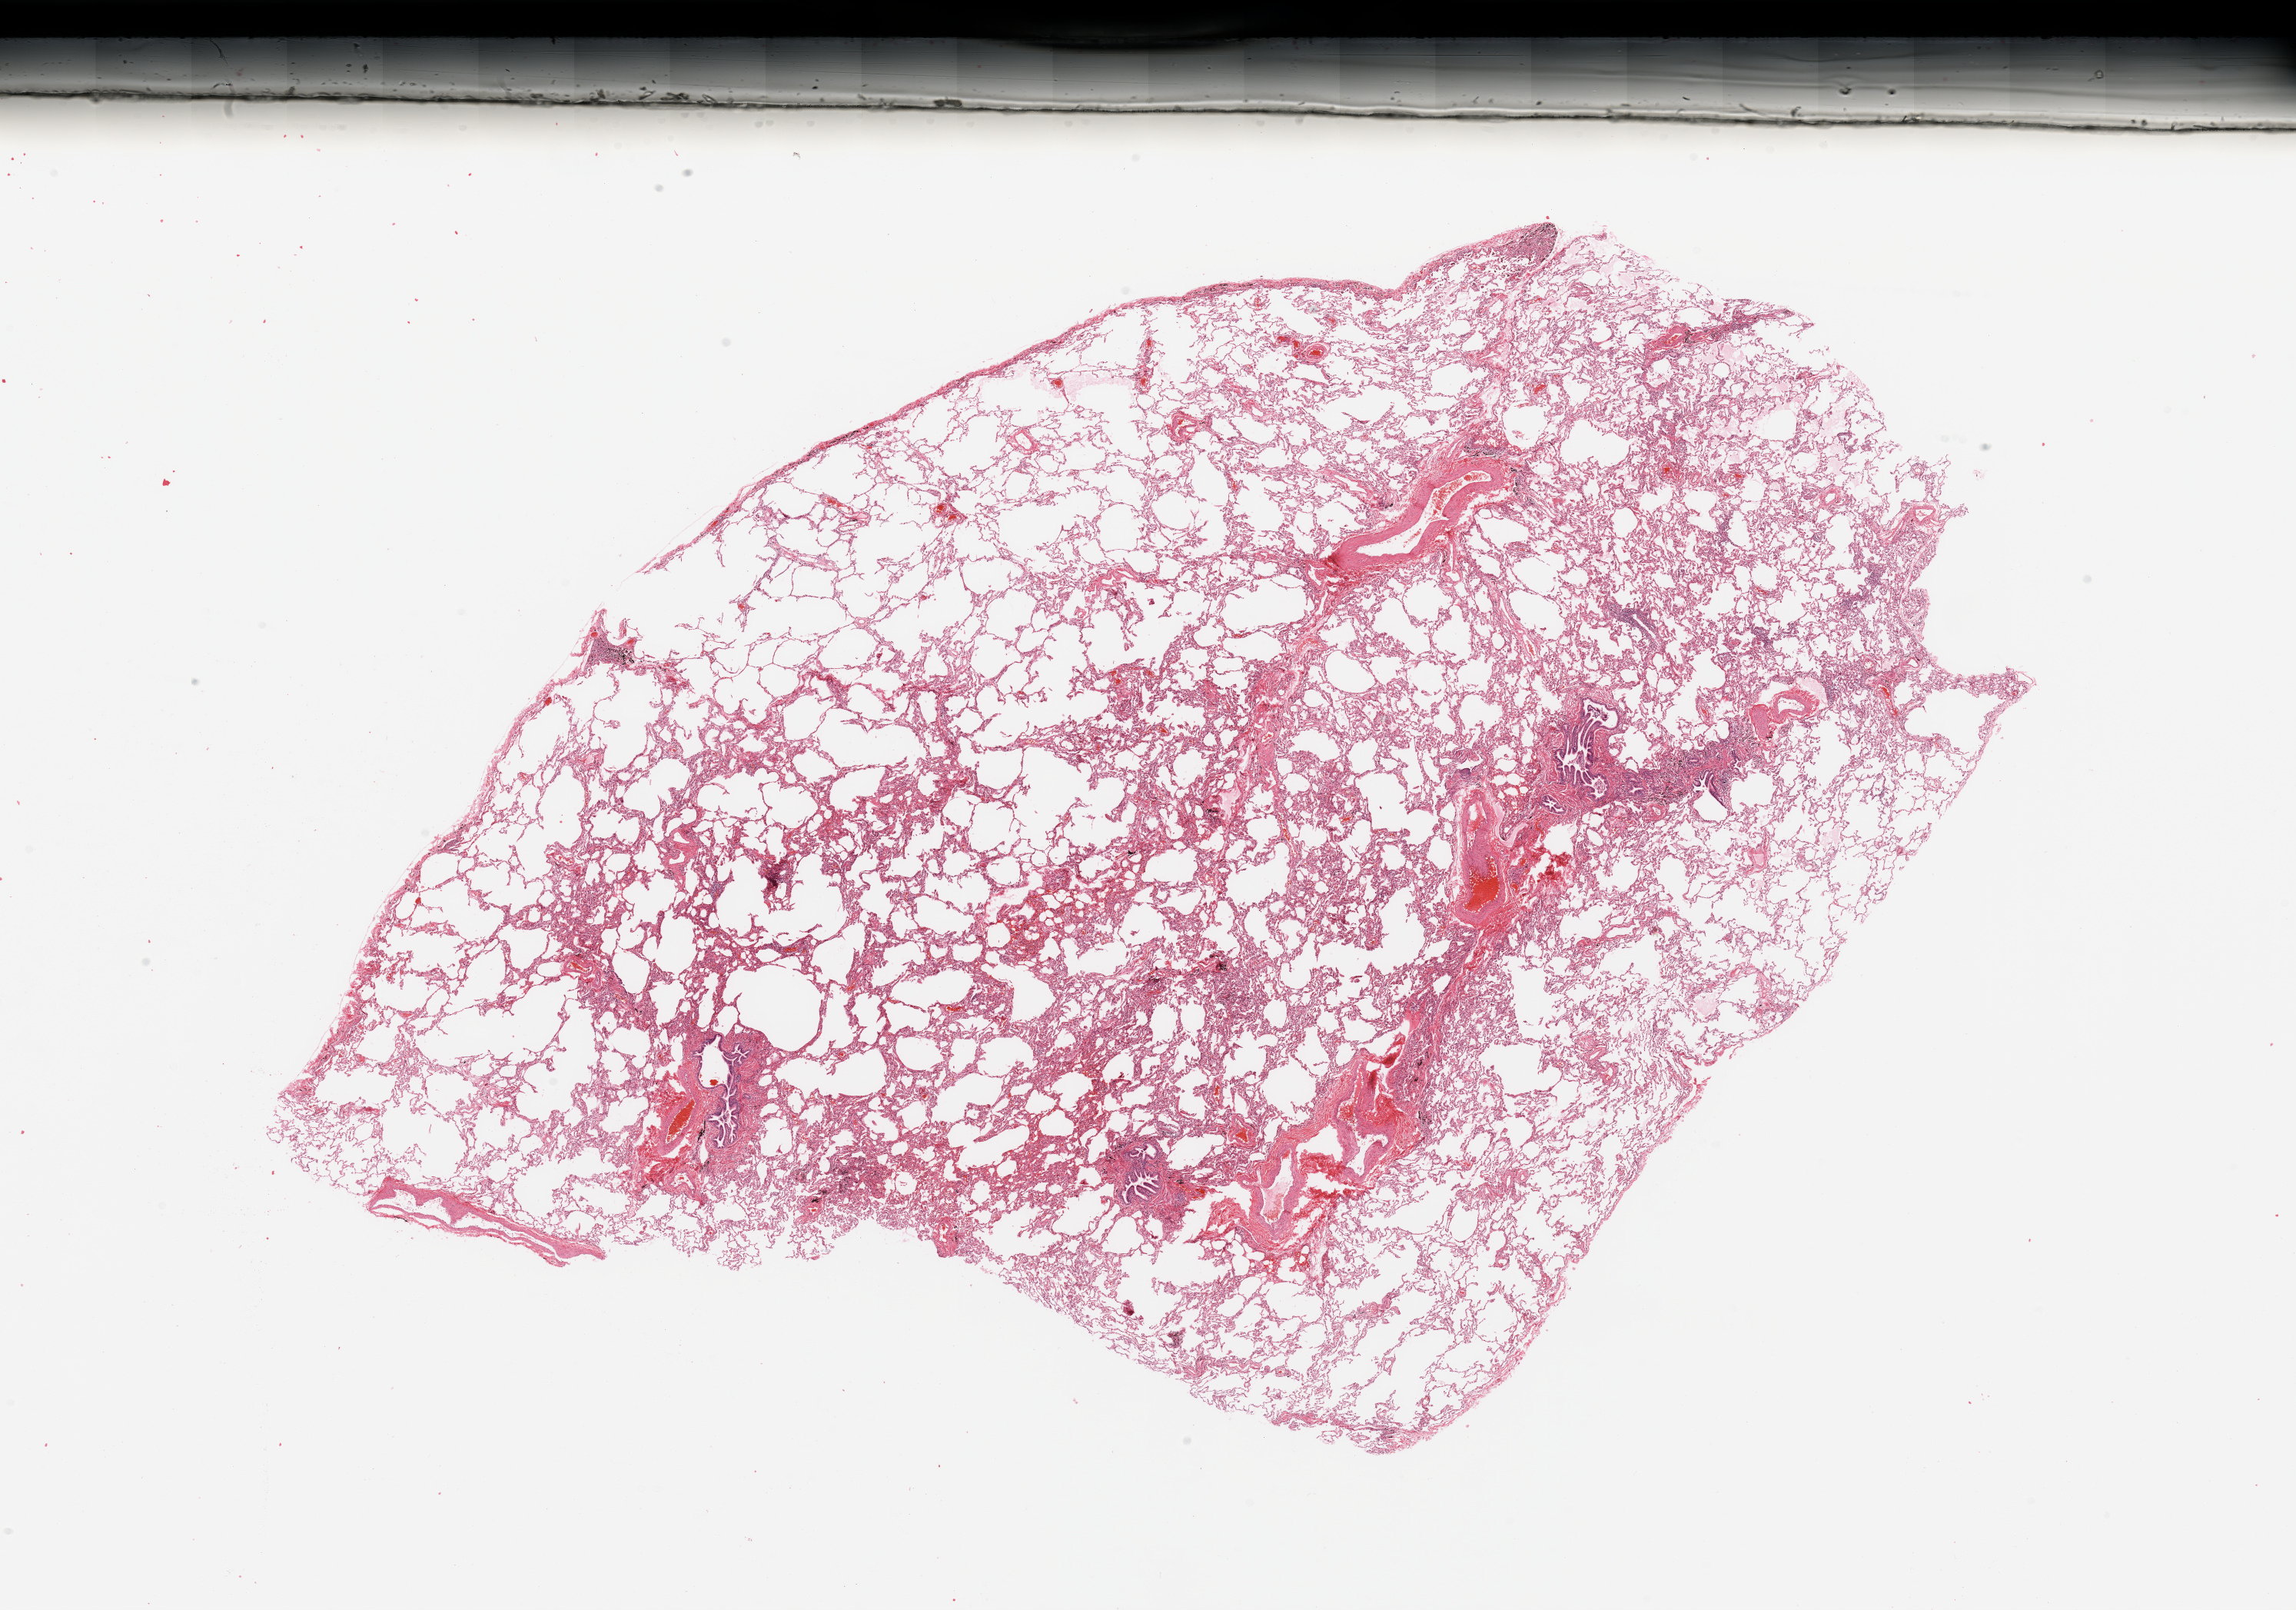
Digitized H&E tissue section (whole slide) — low-resolution overview of the scanned area, about 23.6 x 16.6 mm, normal (non-tumour) tissue sample, sampled site: lung. 67-year-old male patient.
This section: normal (non-tumour) tissue from the same patient. Patient diagnosis: Adenocarcinoma, NOS.